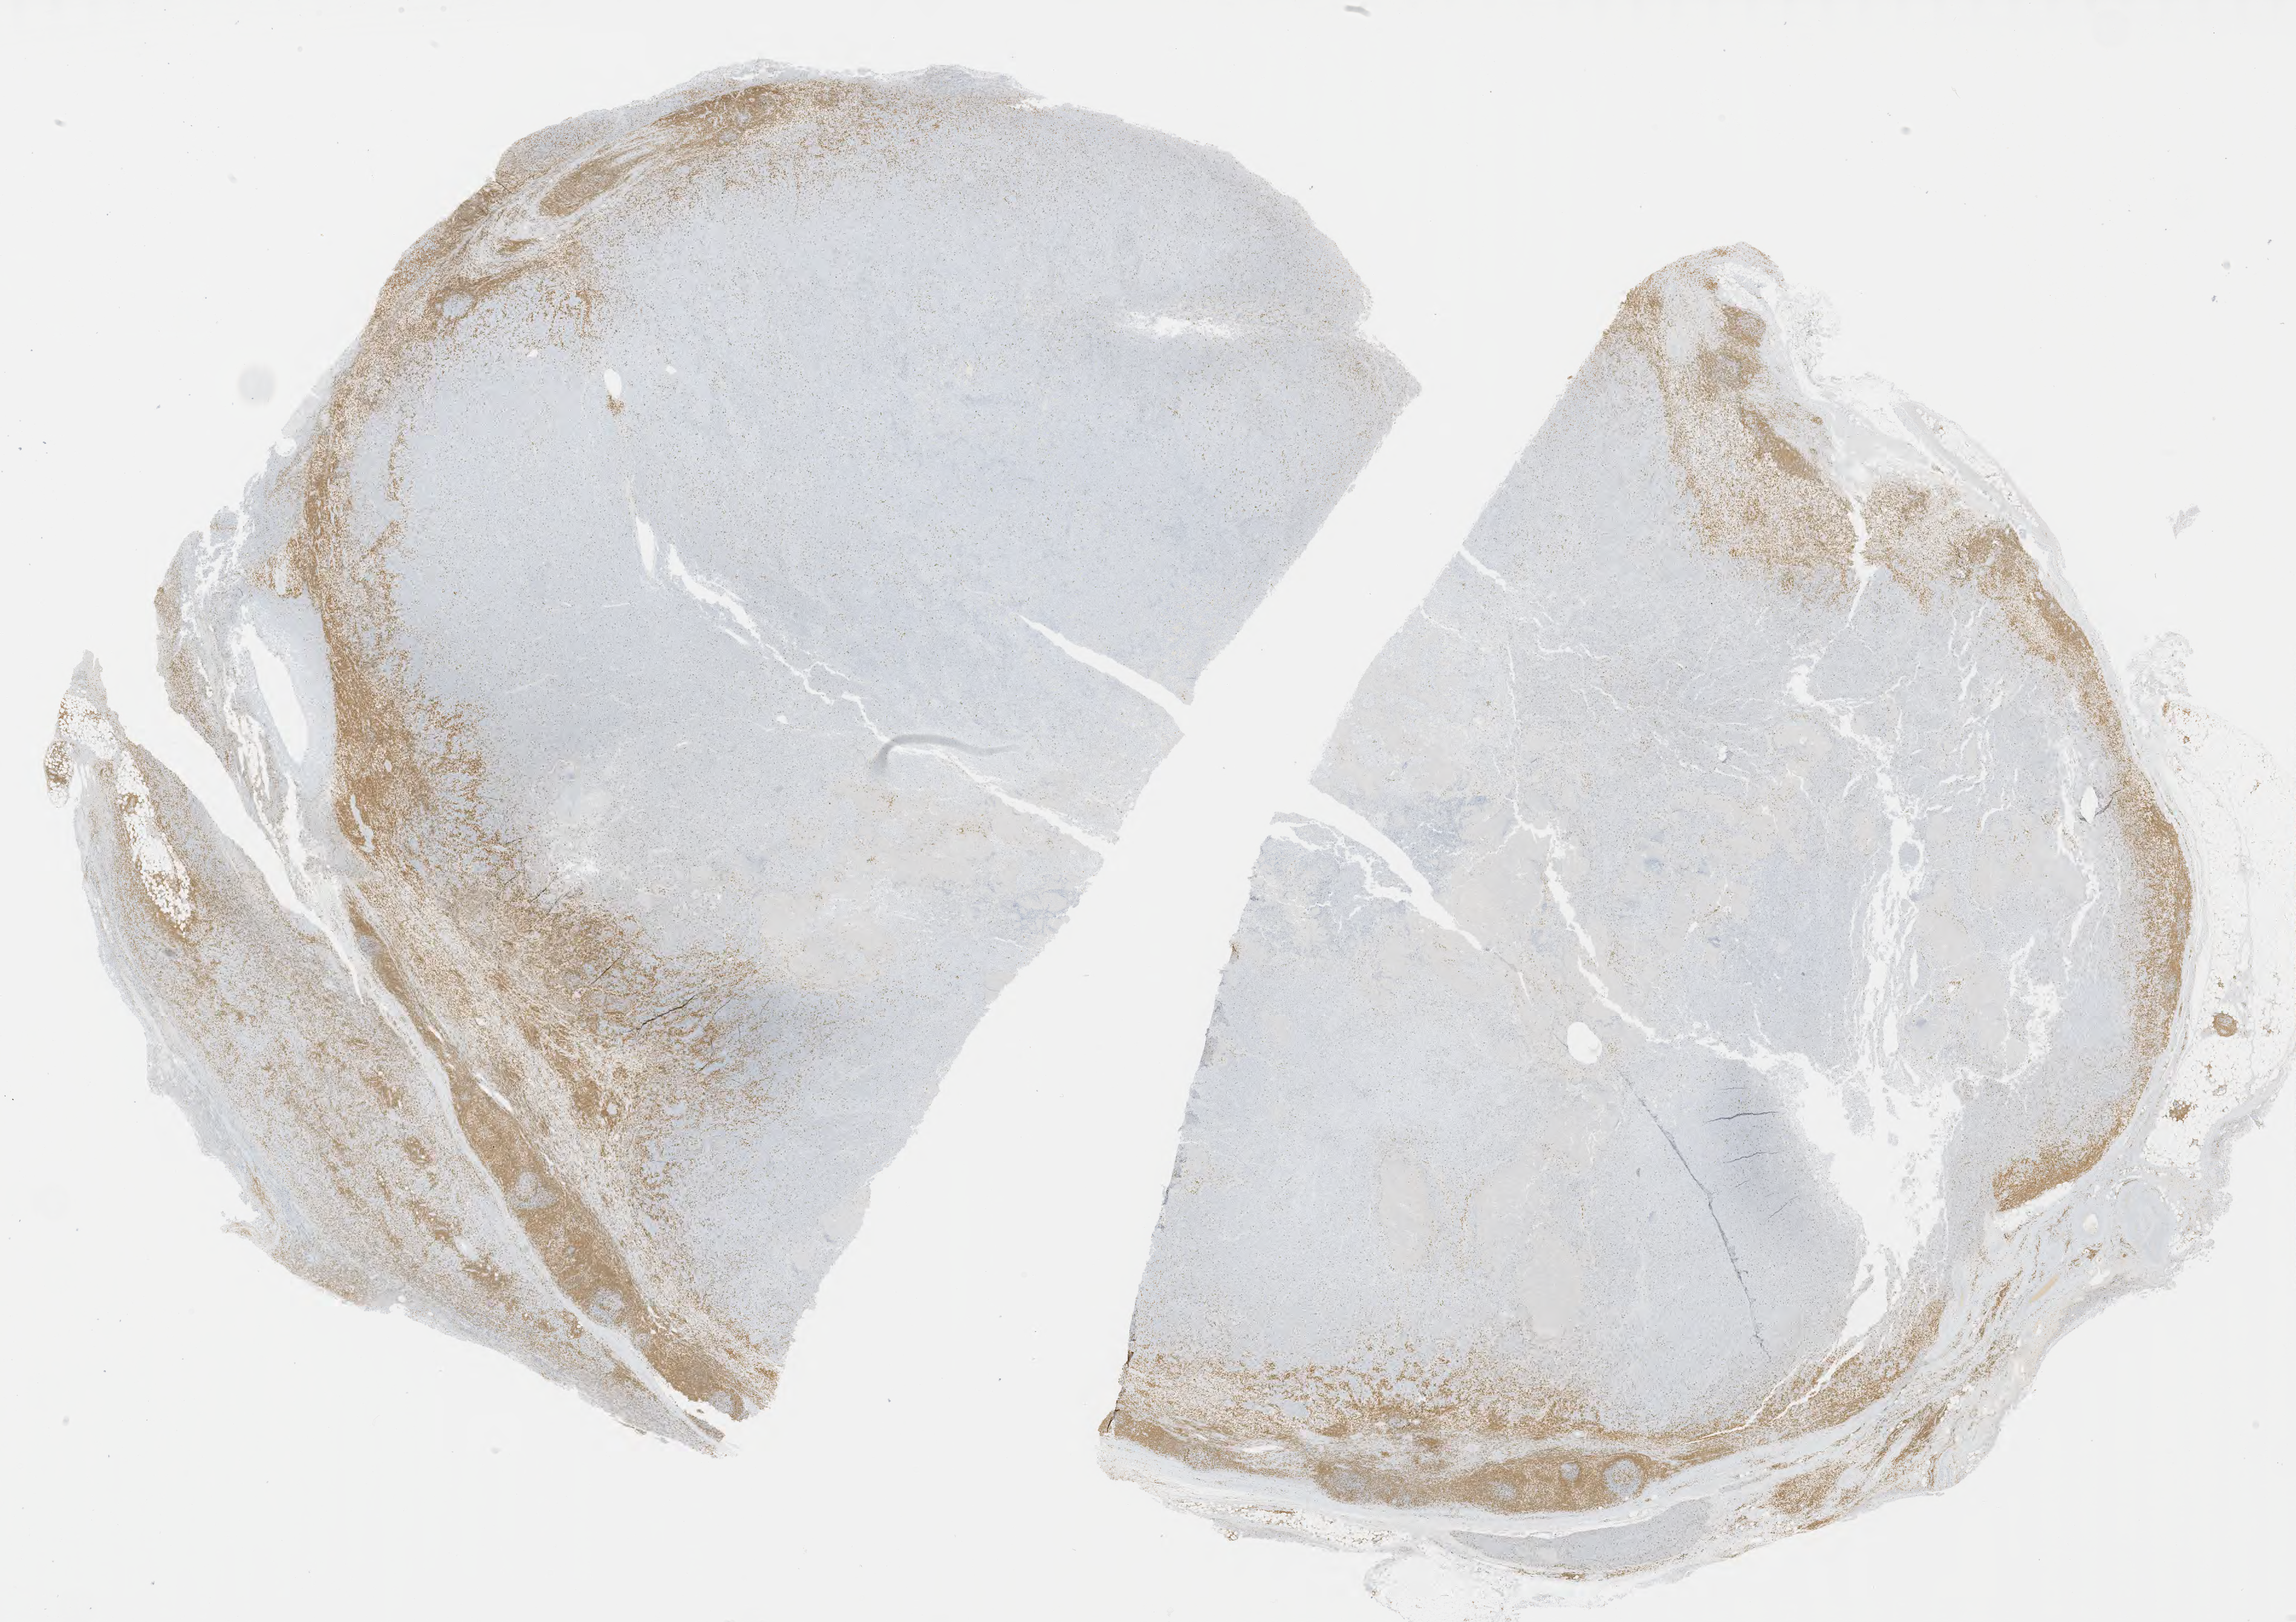
Whole-slide image, immunohistochemical stain for CD3, shown as a low-resolution overview of the whole scanned area (about 30.7 x 21.7 mm); specimen: tumor tissue. Patient male; age 48 years.
* histologic diagnosis: Burkitt lymphoma, NOS